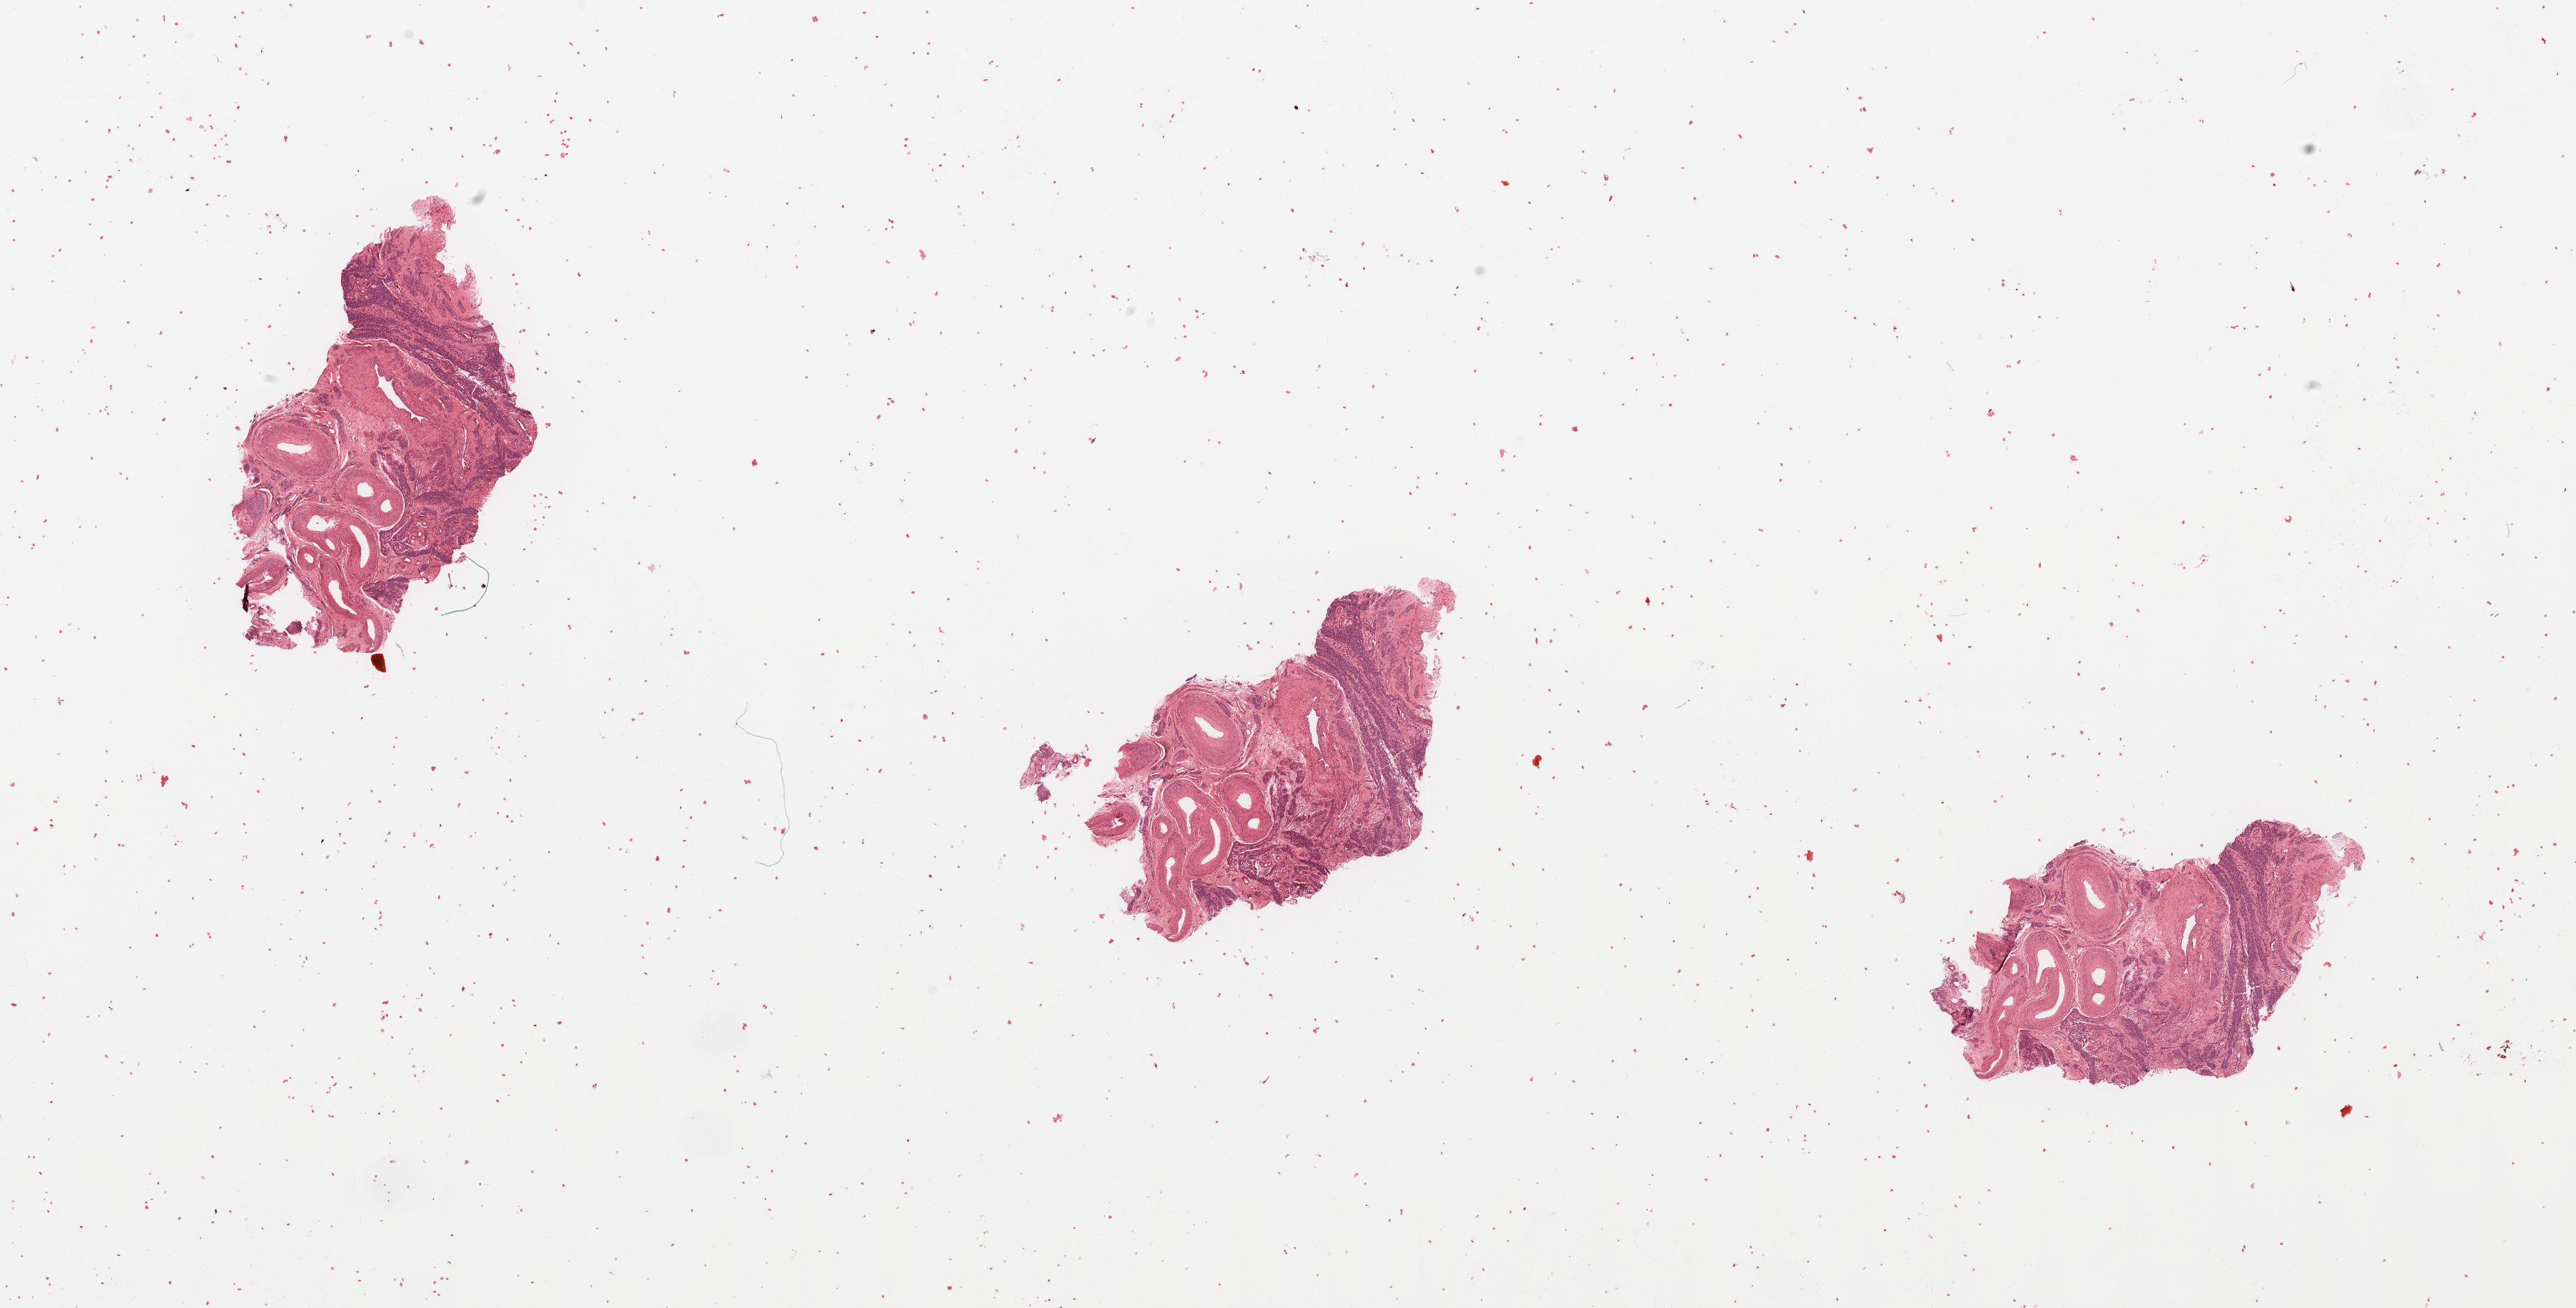
Whole-slide histology image, H&E — whole scanned area (about 28.5 x 14.5 mm, acquisition: 20x scan) shown as a low-resolution overview. Normal (non-tumour) tissue sample, sampled site: uterus. Patient: female, age 66 years.
• this section: normal (non-tumour) tissue from the same patient
• patient diagnosis: Endometrioid adenocarcinoma, NOS